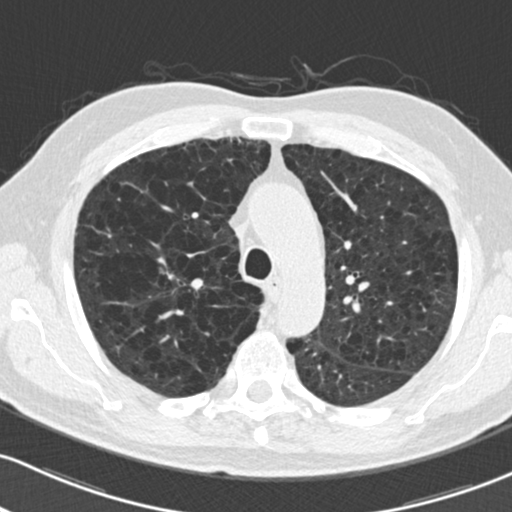
Low-dose screening chest CT, one axial slice. Slice 150 of 204 in the series (ordered by position). Lung window (W 1500 / L -600 HU). 2 mm slice thickness. 512 × 512 image matrix.
Annotated regions visible in this slice (expert manual segmentation):
- lesion 1 (tumor, upper lobe of right lung): bounding box <162,271,179,281> (left, top, right, bottom; pixels)